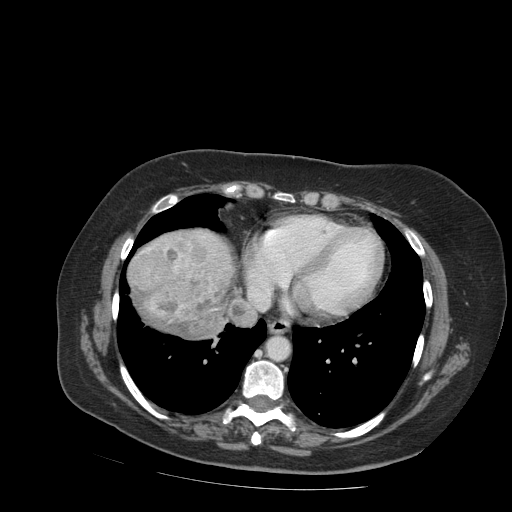
Contrast-enhanced abdominal CT (liver protocol), one axial slice; position 86 of 99 along the scan axis; reconstruction kernel STANDARD; soft-tissue window (W 400 / L 40 HU); 2.5 mm slice thickness; 512 × 512 image matrix, field of view 400 × 400 mm. From the clinical record (not read from this slice): diagnosis: hepatocellular carcinoma (patient treated with transarterial chemoembolisation; whether this scan precedes or follows treatment is not stated here); TNM stage (as recorded): Stage-IVB; Child-Pugh class: A; tumour differentiation: moderately differentiated.
Annotated regions visible in this slice (semi-automatically segmented with operator editing):
- liver parenchyma outside the tumour (the mass and vessels are separate outlines, so this box may not span the whole liver): box from (x=128, y=228) to (x=248, y=338) px
- mass: (x=132, y=244)–(x=236, y=335)